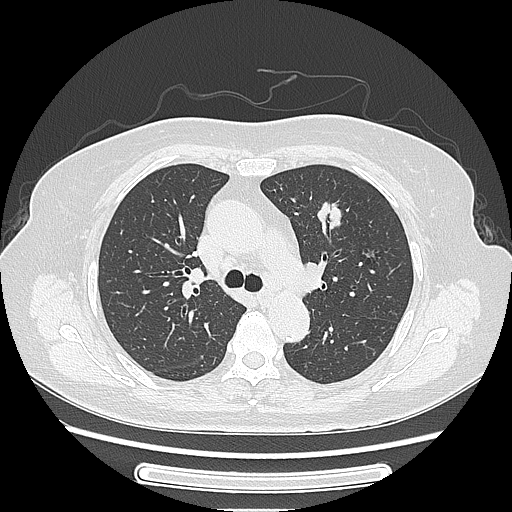
Chest CT, one axial slice. Position 161 of 227 along the scan axis. Reconstruction kernel LUNG. 120 kVp. Lung window (W 1500 / L -600 HU). 1.25 mm slice thickness. 512 × 512 image matrix, field of view 363 × 363 mm. Patient: female, 77 years. From the clinical record (not read from this slice): clinical TNM (as recorded): T1c N3 M0; histopathological grade: G2-3.
Outlined on this slice (rectangle marked by the reading radiologist):
- lung tumour (recorded histology: adenocarcinoma): box from (x=315, y=198) to (x=361, y=245) px